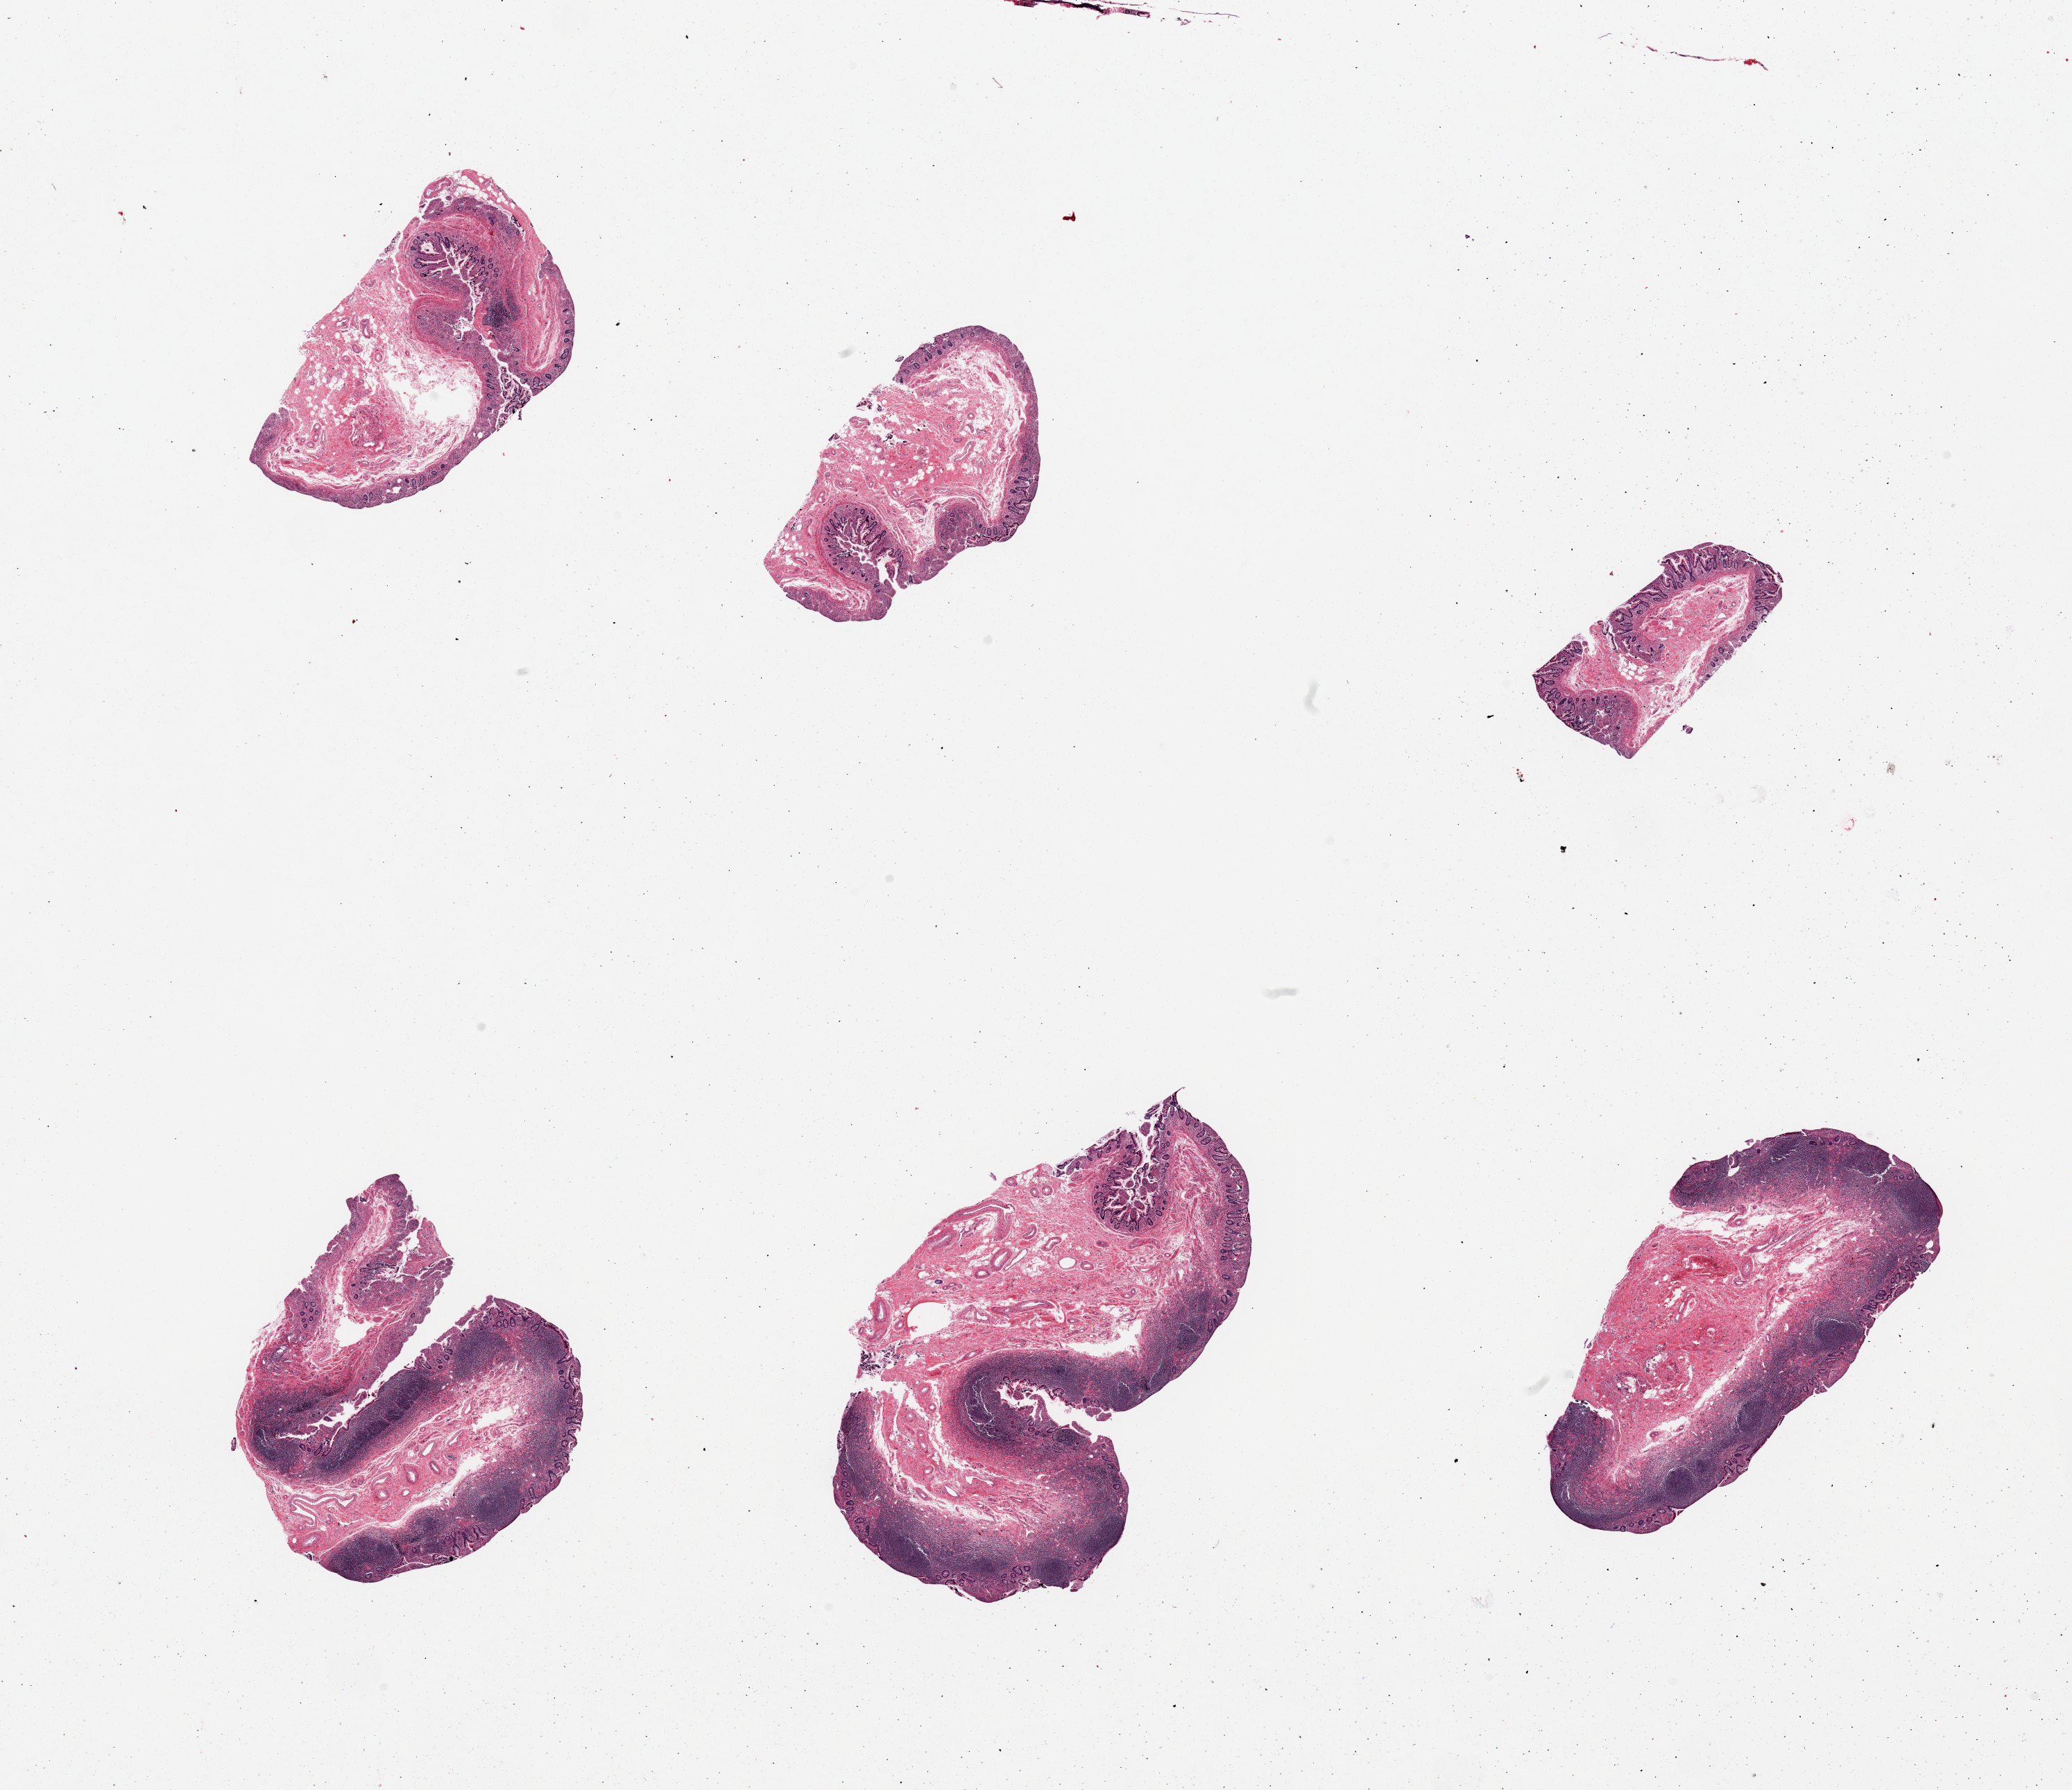
Hematoxylin and eosin (H&E) whole-slide image, brightfield, shown as a low-resolution overview of the whole scanned area (about 23.6 x 20.4 mm, from a 20x scan). PAXgene-fixed, paraffin-embedded tissue. Sampled site (target tissue): ileum. Donor tissue sample. Donor sex: female.
- pathologist's review note for this sample: 6 pieces, well preserved; lymphoid aggregates 30-40% of tissue